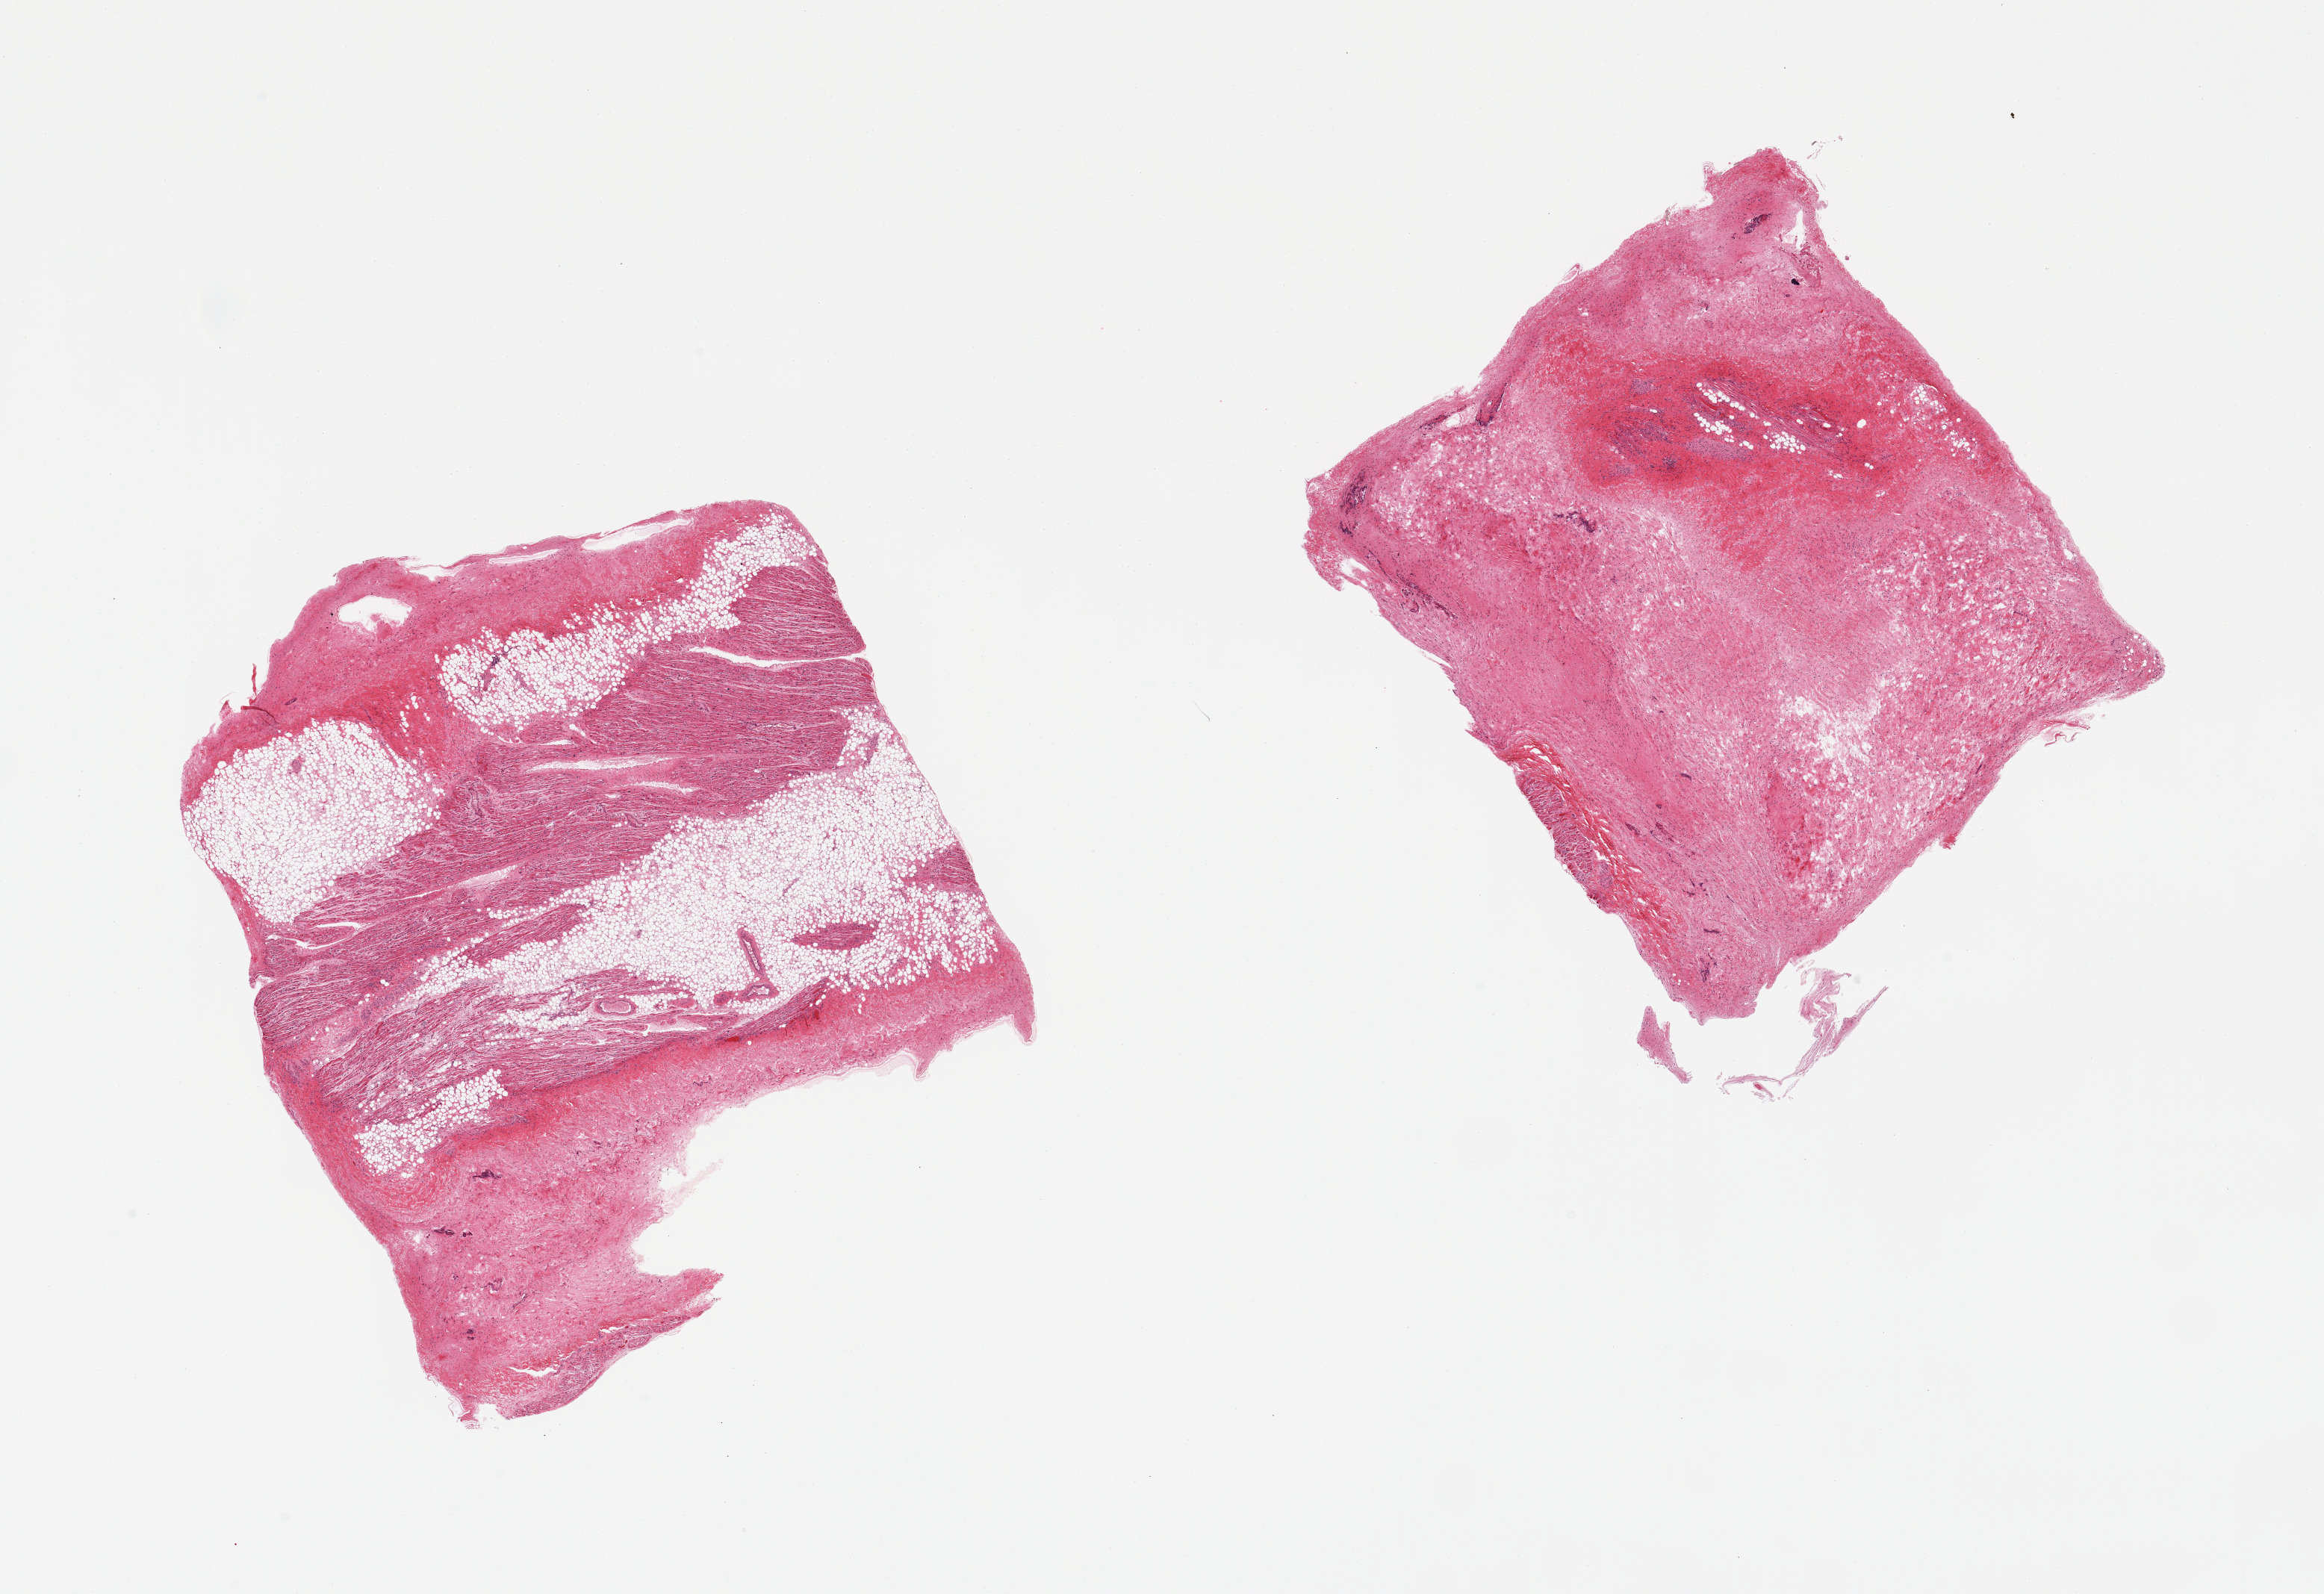
Digitized haematoxylin and eosin-stained section, low-resolution overview of the scanned area, about 24.6 x 16.9 mm, PAXgene-fixed, paraffin-embedded tissue, section of auricular appendage (target tissue), tissue donor sample. Male donor.
Pathologist's review note for this sample: 2 pieces; one piece is nearly entierly fibrous, second is 70% fibrous and fatty.